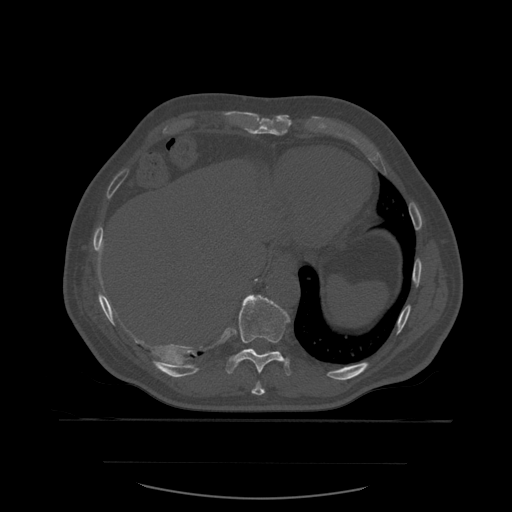
CT including the spine, one axial slice. Slice 318 of 590 in the series (ordered by position). Bone window (W 1800 / L 400 HU). 1.25 mm slice thickness. 512 × 512 image matrix. Patient age 71 years. Case-level facts recorded for this patient, not image findings: primary cancer: lung.
Annotated regions visible in this slice (semi-automatic segmentation, software-assisted and operator-edited):
- T10 vertebra: box from (x=226, y=295) to (x=292, y=376) px
- T9 vertebra: (x=252, y=382)–(x=266, y=396)